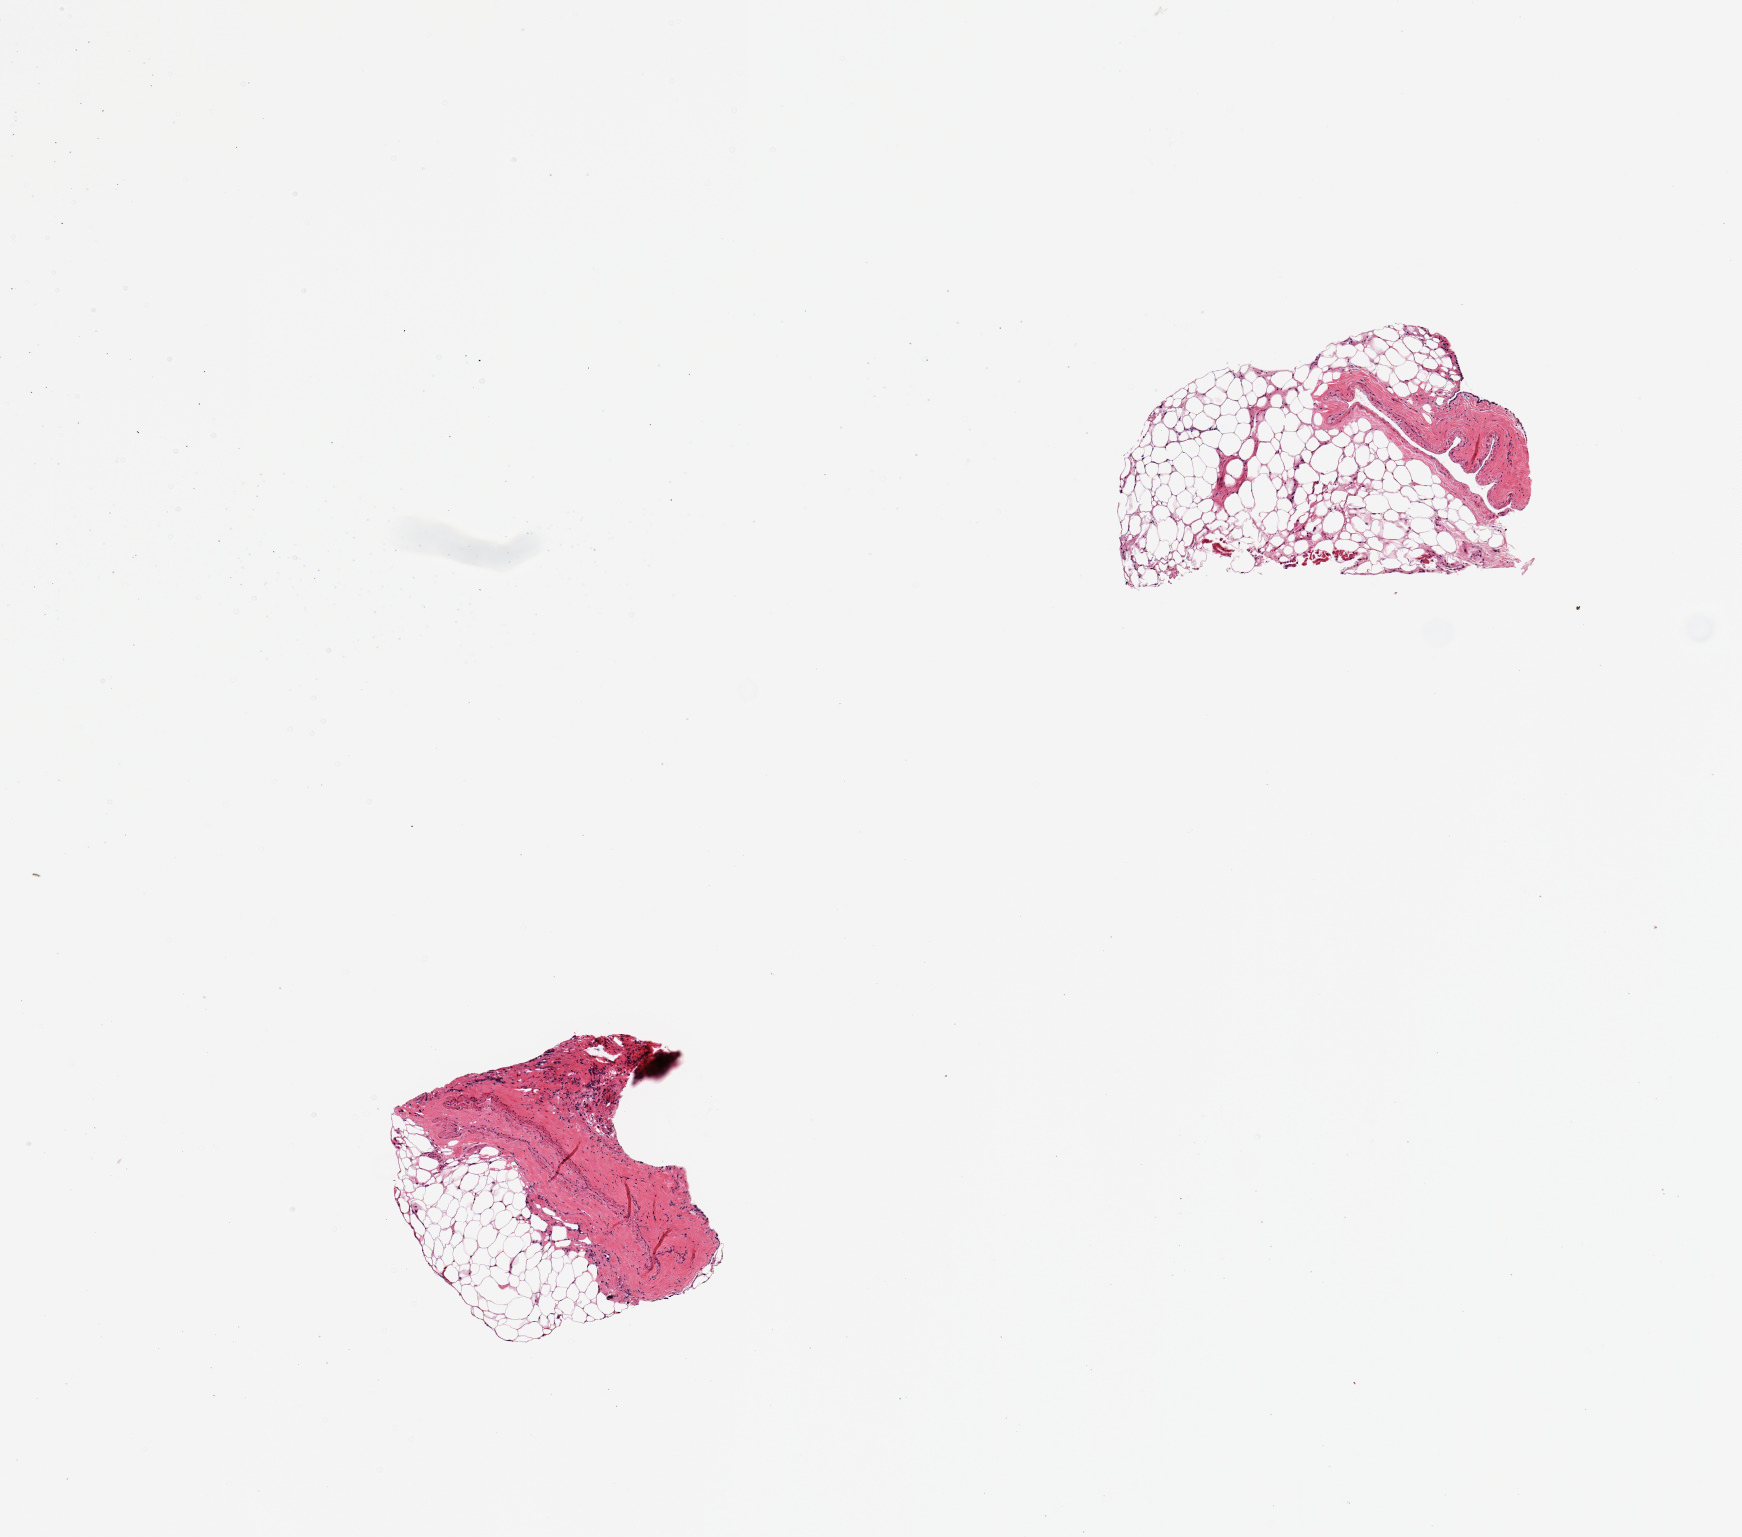
Haematoxylin and eosin whole-slide image — whole scanned area (about 6.9 x 6.1 mm, slide scanned at 20x) shown as a low-resolution overview. PAXgene-fixed, paraffin-embedded tissue. Sampled site (target tissue): coronary artery. Tissue donor sample. Donor sex: female.
* review note (as recorded): 2 pieces; 40 & 80% external fat